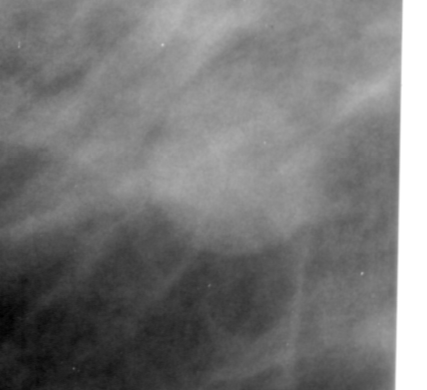
Region of interest cut from a scanned film mammogram (one marked finding), left breast, MLO view, BI-RADS breast density category 4 (scale 1–4).
- Mass, shape round, margins circumscribed; BI-RADS assessment category 4; pathology (as recorded): benign.